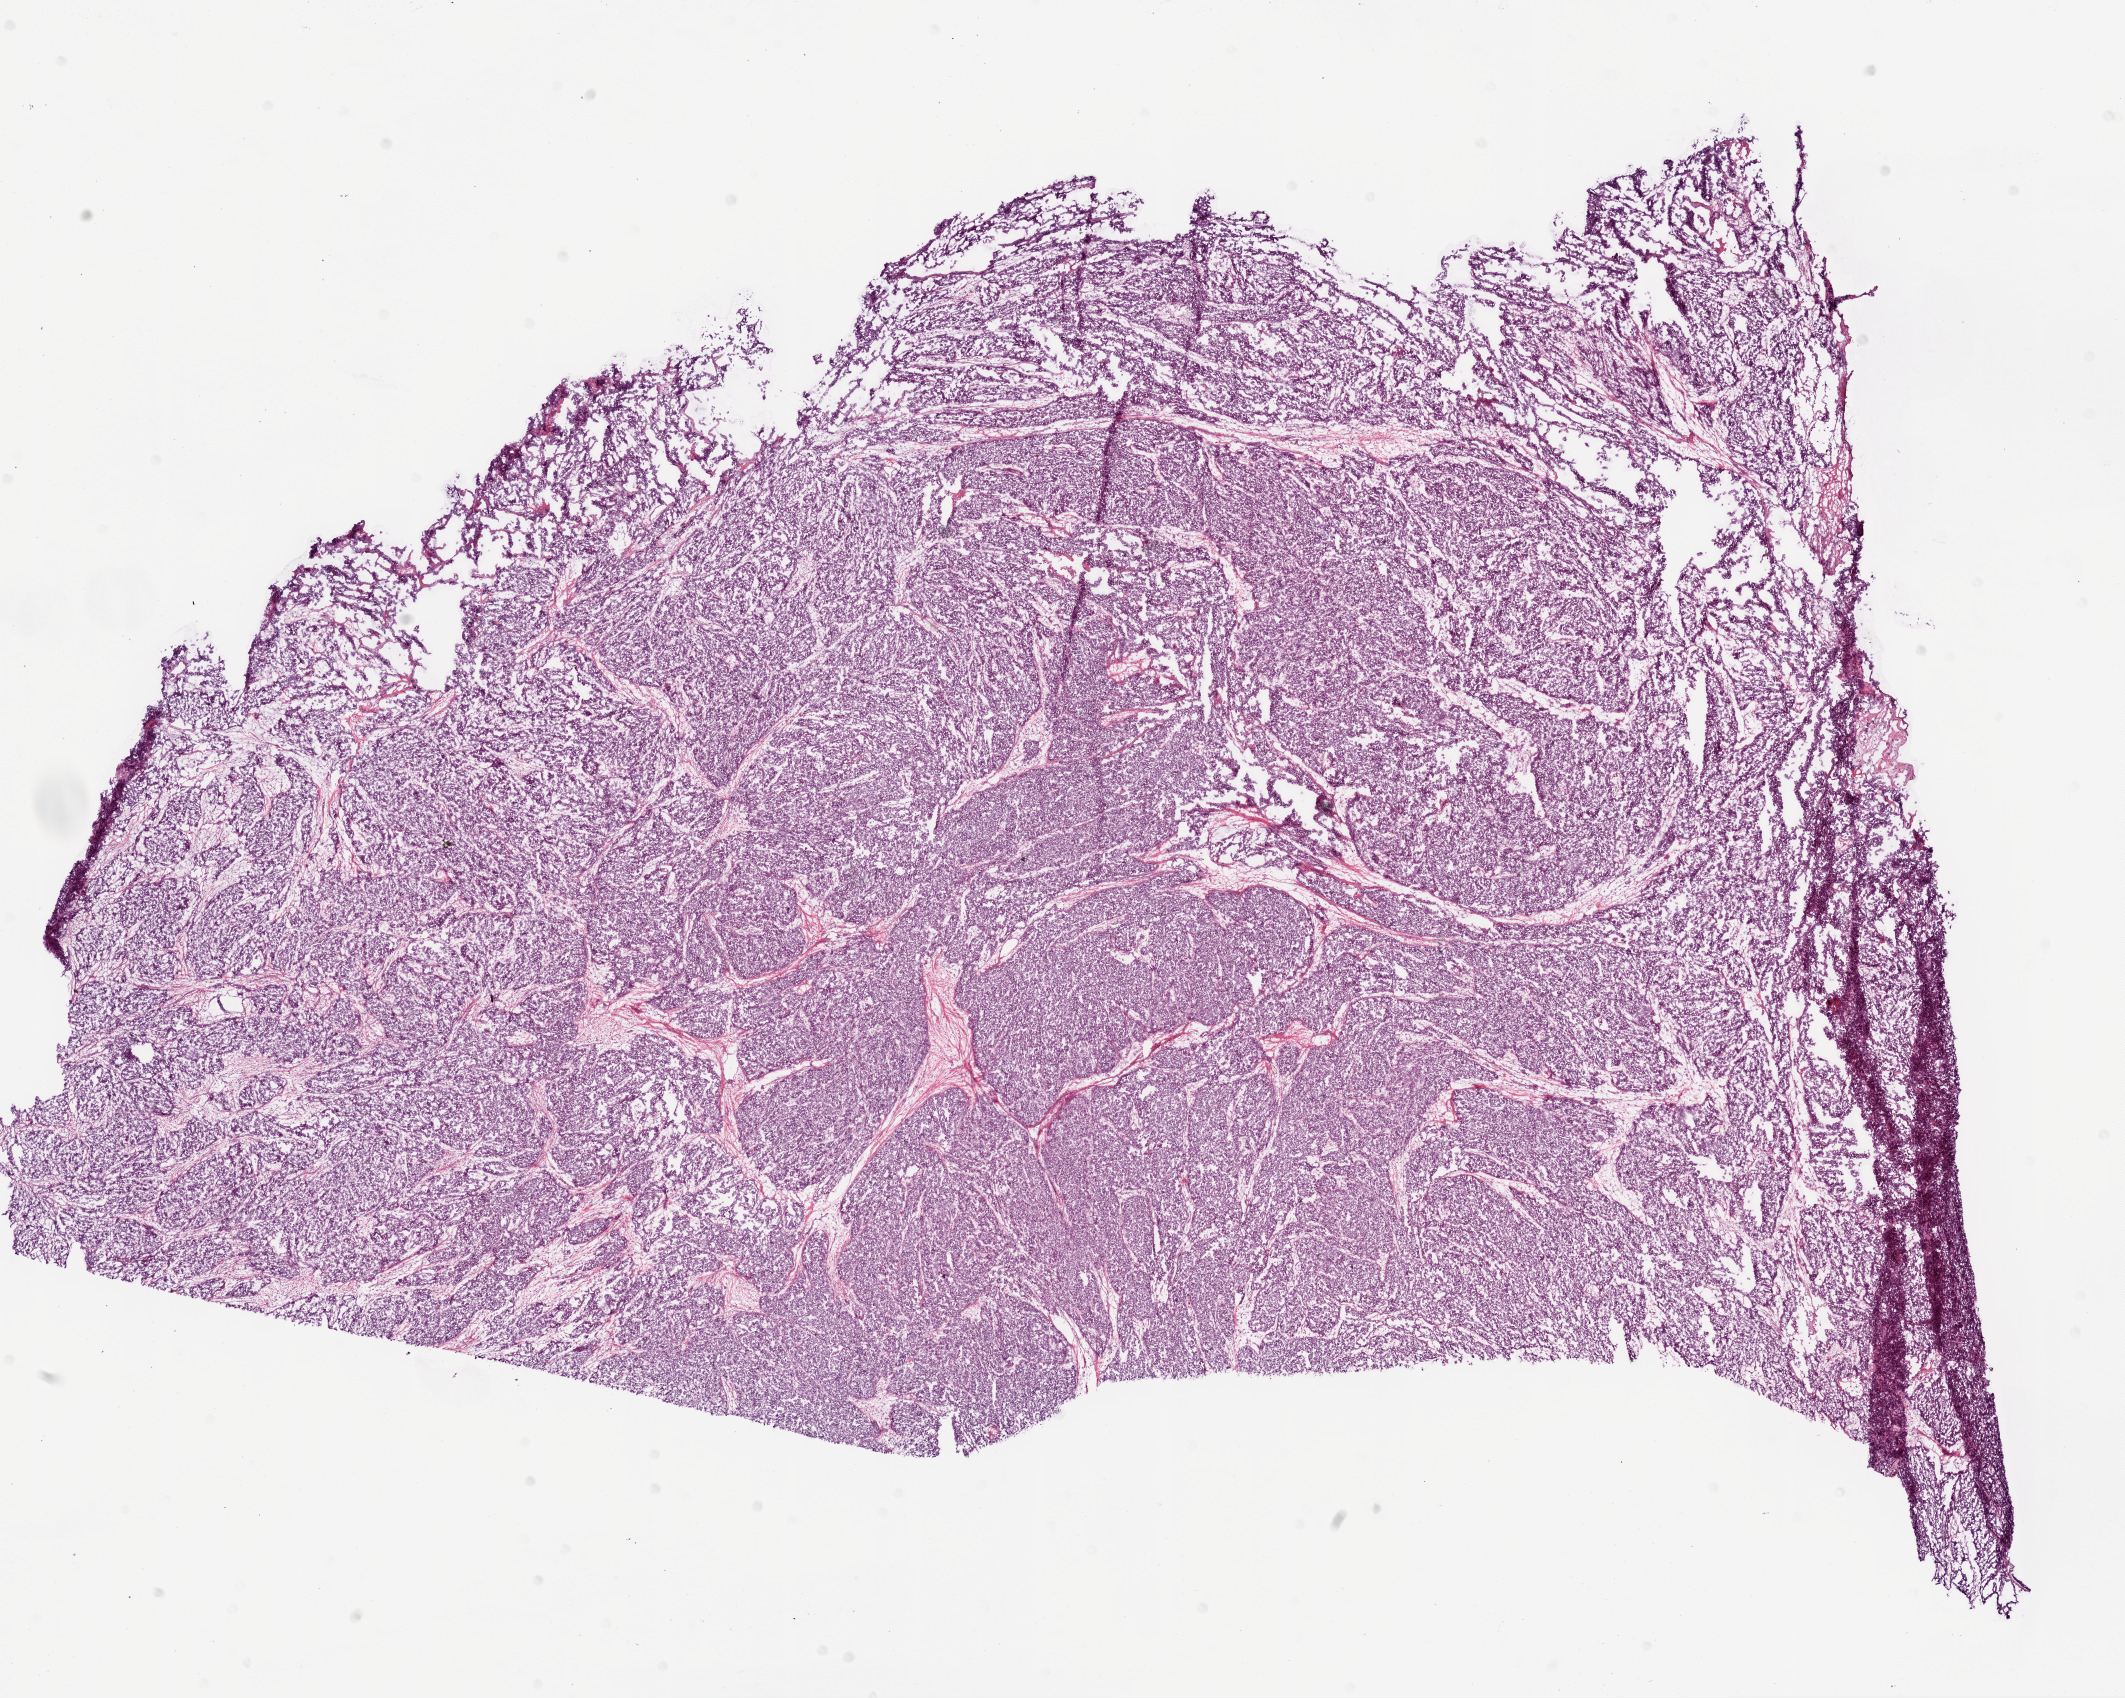
Whole-slide histology image, H&E — a low-resolution overview of the entire scanned area, about 17.1 x 13.6 mm. Frozen section from the bottom of the tissue portion. Ovary, primary tumour sample. Female, age 73 years at initial diagnosis. Slide review estimates, as recorded: tumour cells 98%, tumour nuclei 95%.
Diagnosis: Serous cystadenocarcinoma, NOS.